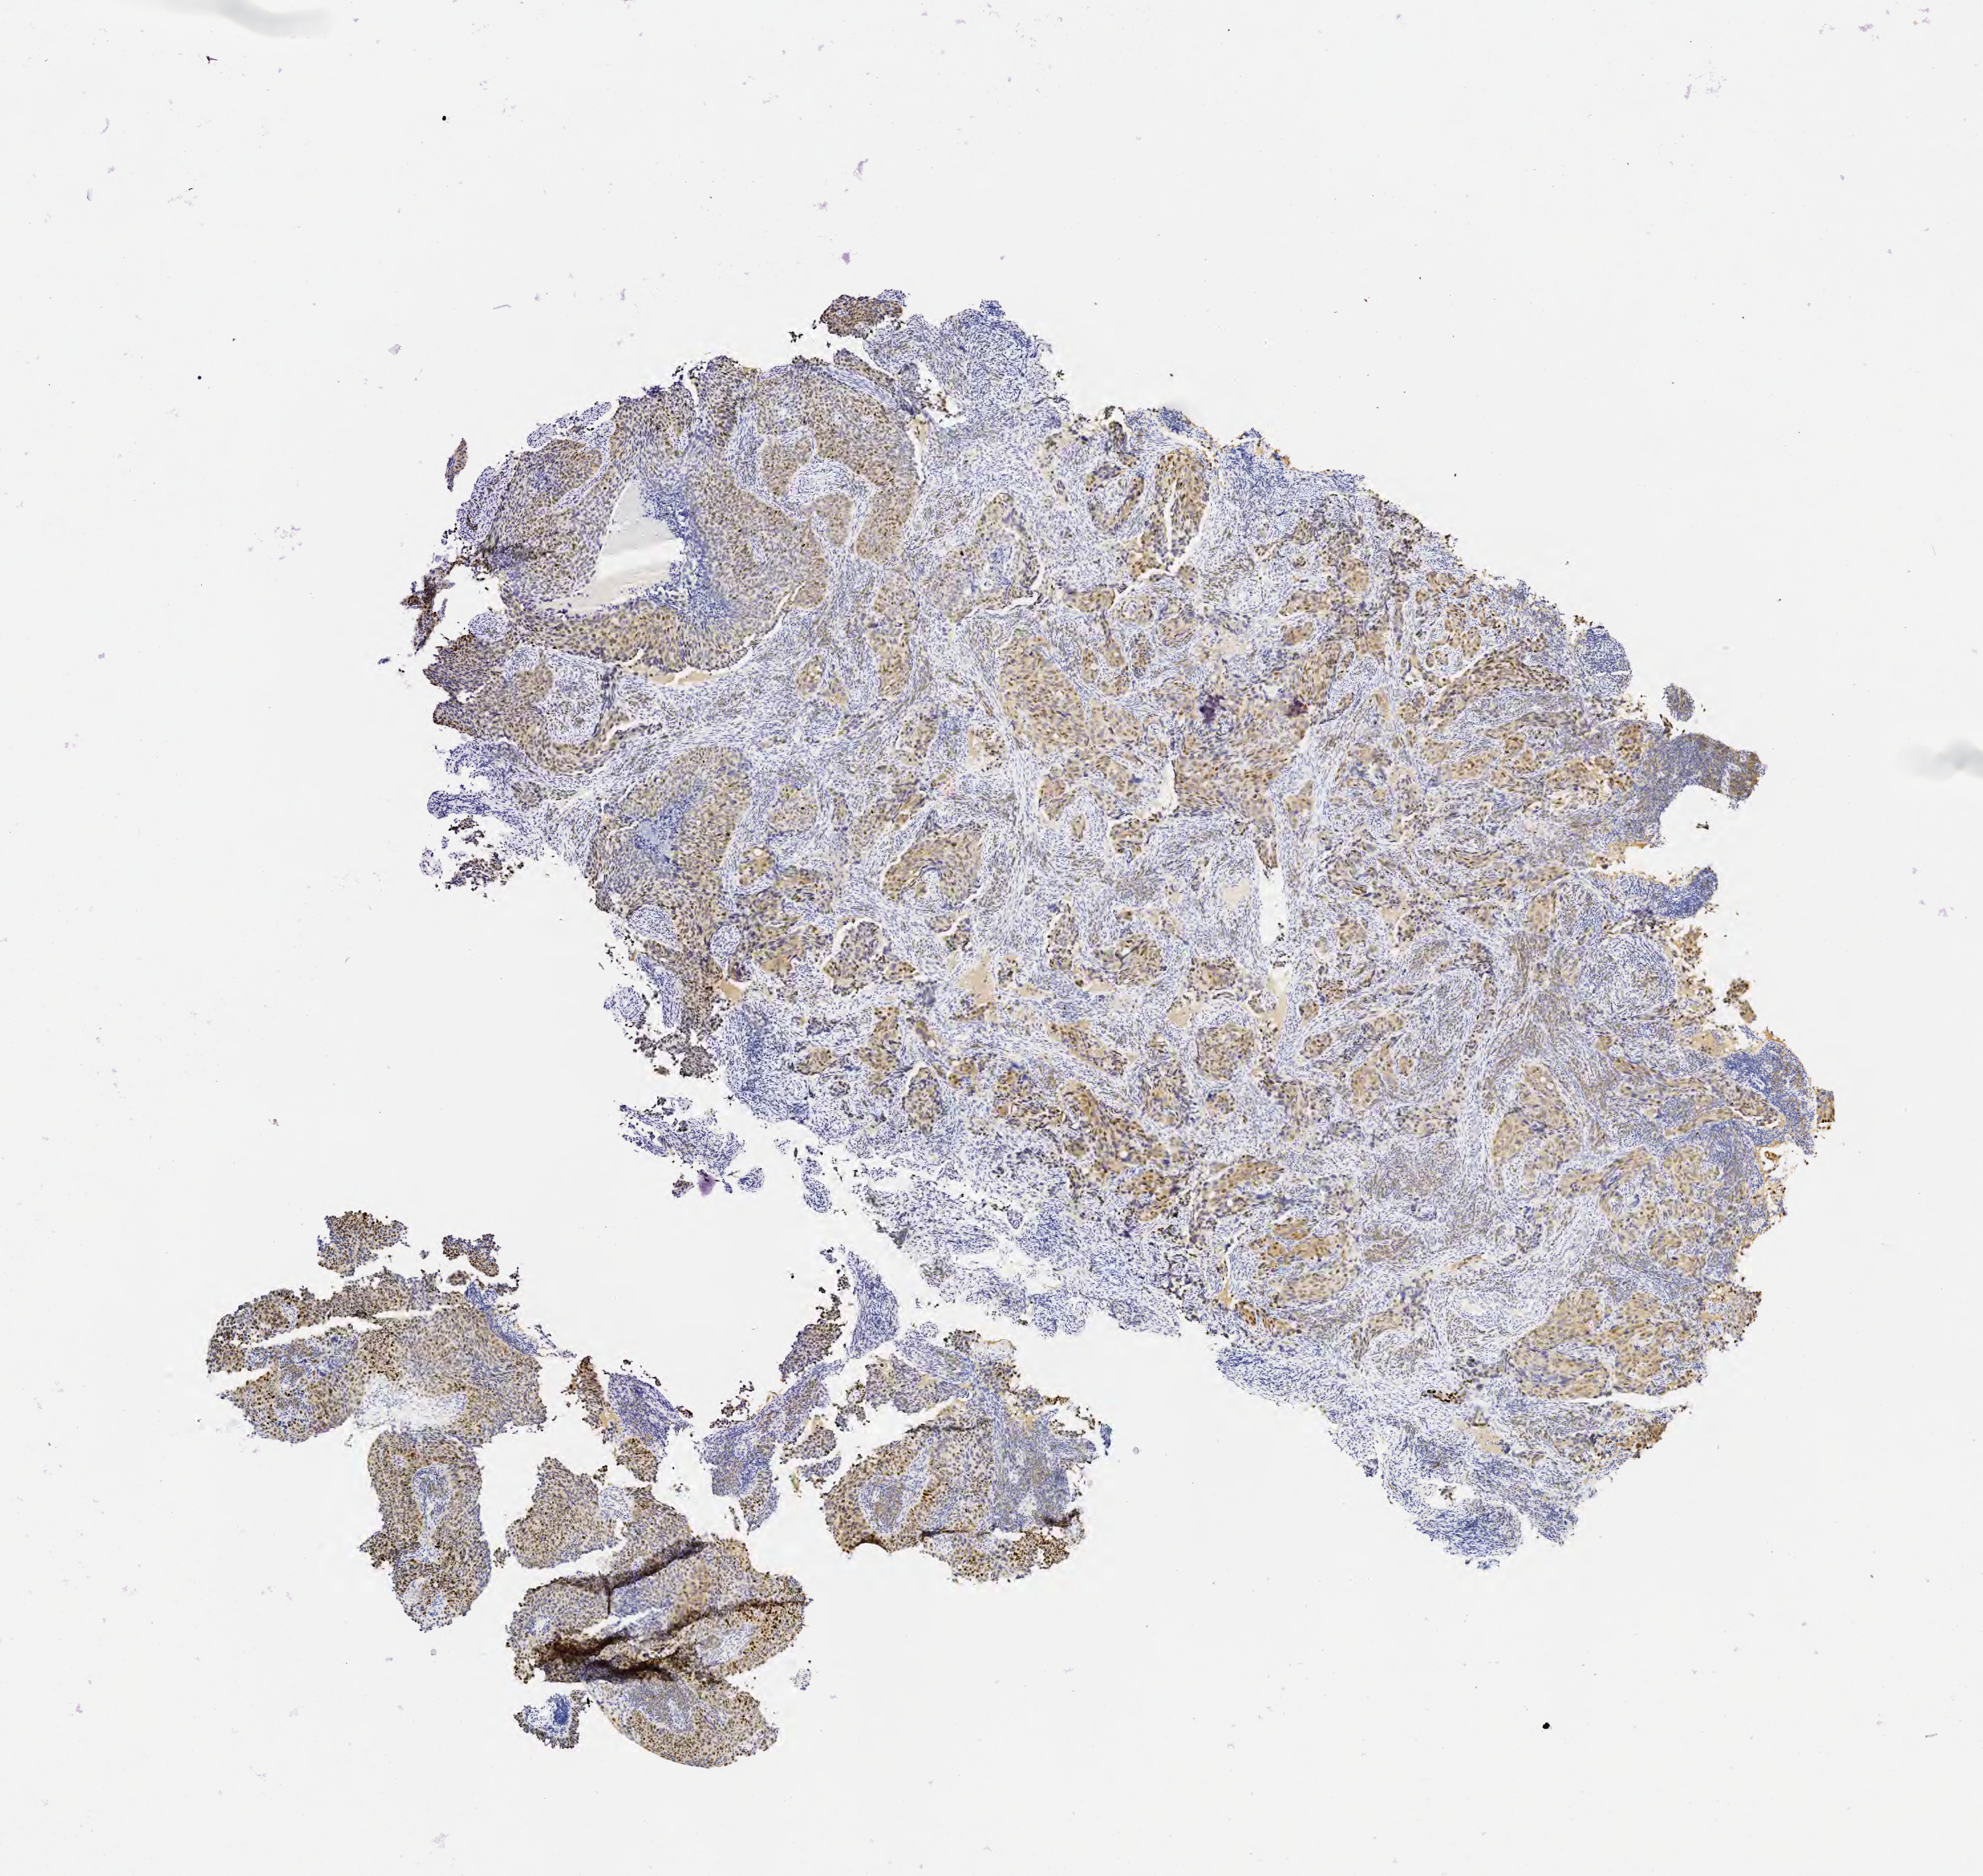
IHC for p63, whole-slide image — a low-resolution overview of the entire scanned area, about 6.0 x 5.7 mm, specimen: tumor tissue, site: cervix. Female patient, 47 years old.
Diagnosis: Squamous cell carcinoma, large cell, nonkeratinizing, NOS.